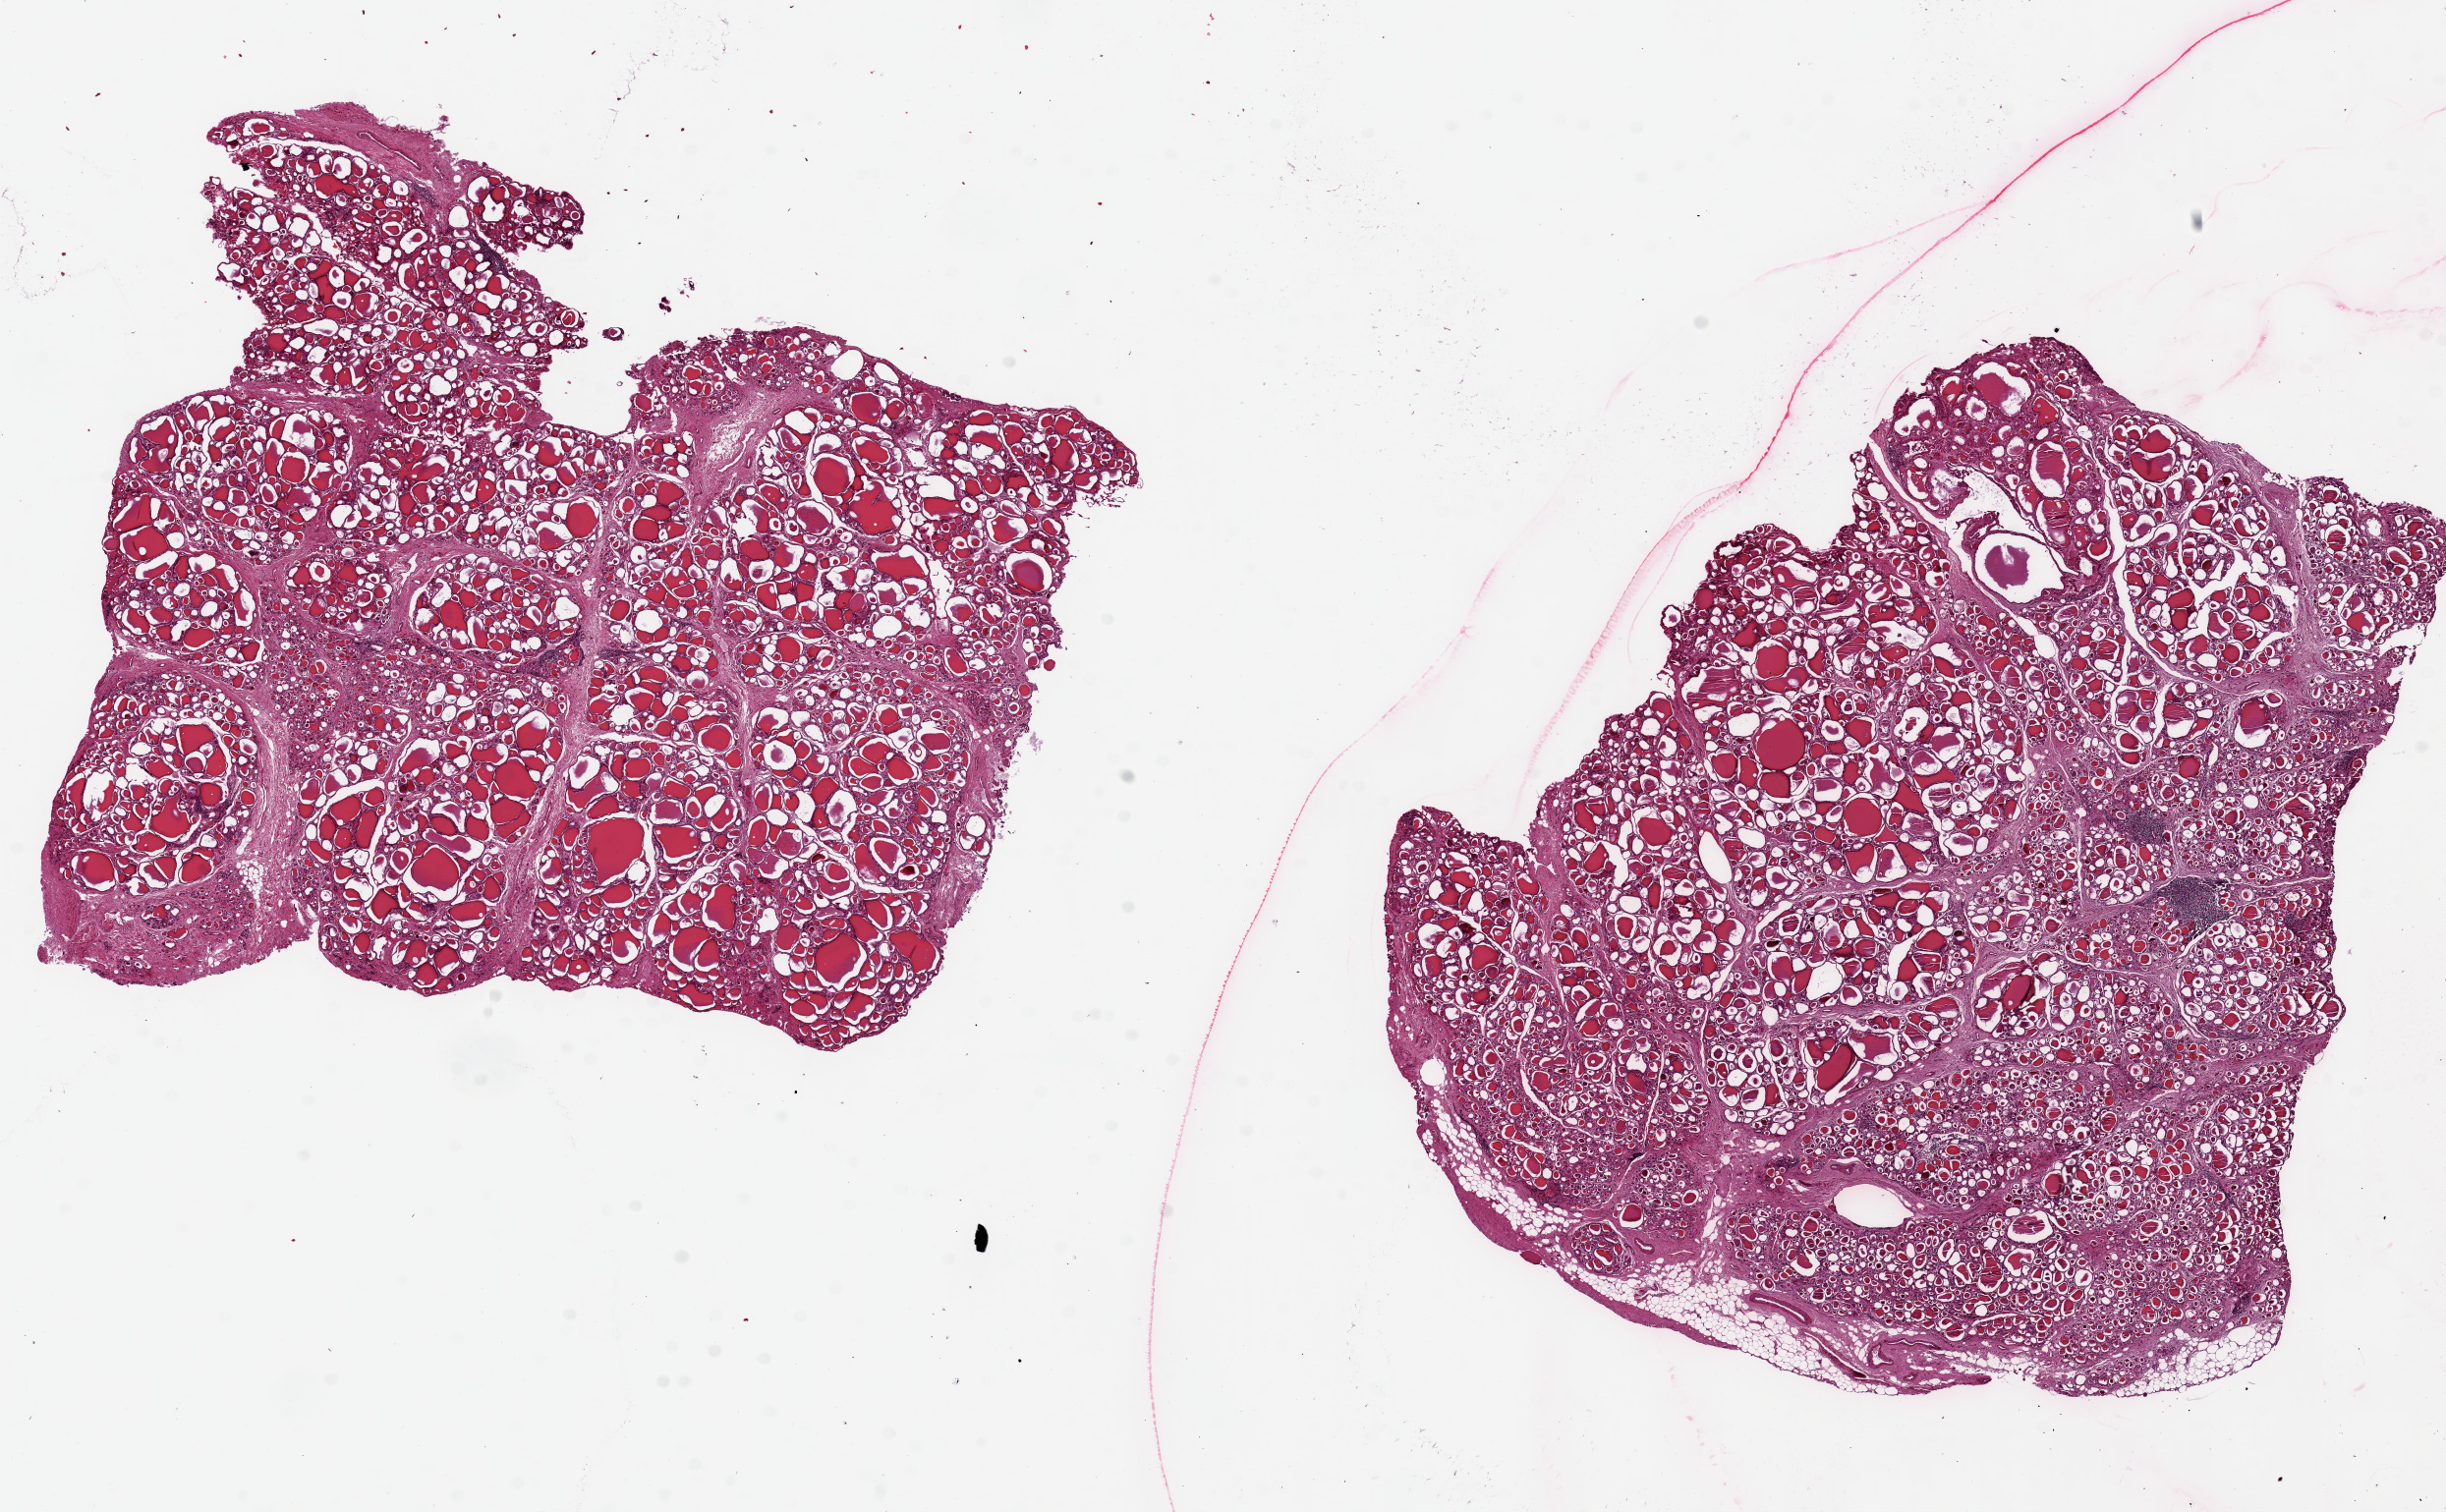
Whole-slide image, hematoxylin and eosin (H&E) stain, a low-resolution overview of the entire scanned area, about 19.7 x 12.2 mm, PAXgene-fixed paraffin-embedded (PFPE) section, section of thyroid (target tissue), donor tissue sample. Donor sex: male.
Reviewer comment on this tissue sample: 2 pieces `7x7mm, diffuse micronodular goitre and Hashimoto's thyroiditis.